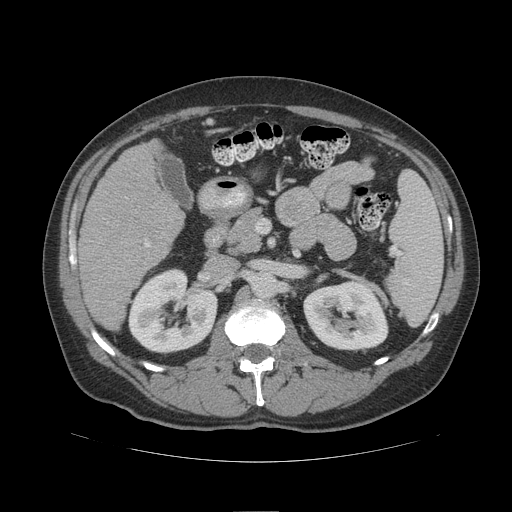
Contrast-enhanced abdominal CT (liver protocol), one axial slice; slice 51 of 109 in the series (ordered by position); soft-tissue window (W 400 / L 40 HU); 512 × 512 image matrix. Case-level facts recorded for this patient, not image findings: diagnosis: hepatocellular carcinoma (patient treated with transarterial chemoembolisation; whether this scan precedes or follows treatment is not stated here); TNM stage (as recorded): Stage-IIIB; Child-Pugh class: A; tumour nodularity: multinodular.
Structures marked on this image (semi-automatic segmentation, software-assisted and operator-edited):
- liver parenchyma outside the tumour (the mass and vessels are separate outlines, so this box may not span the whole liver): bounding box [x1, y1, x2, y2] px = [78, 140, 184, 330]
- liver vessels: [145, 243, 150, 247]